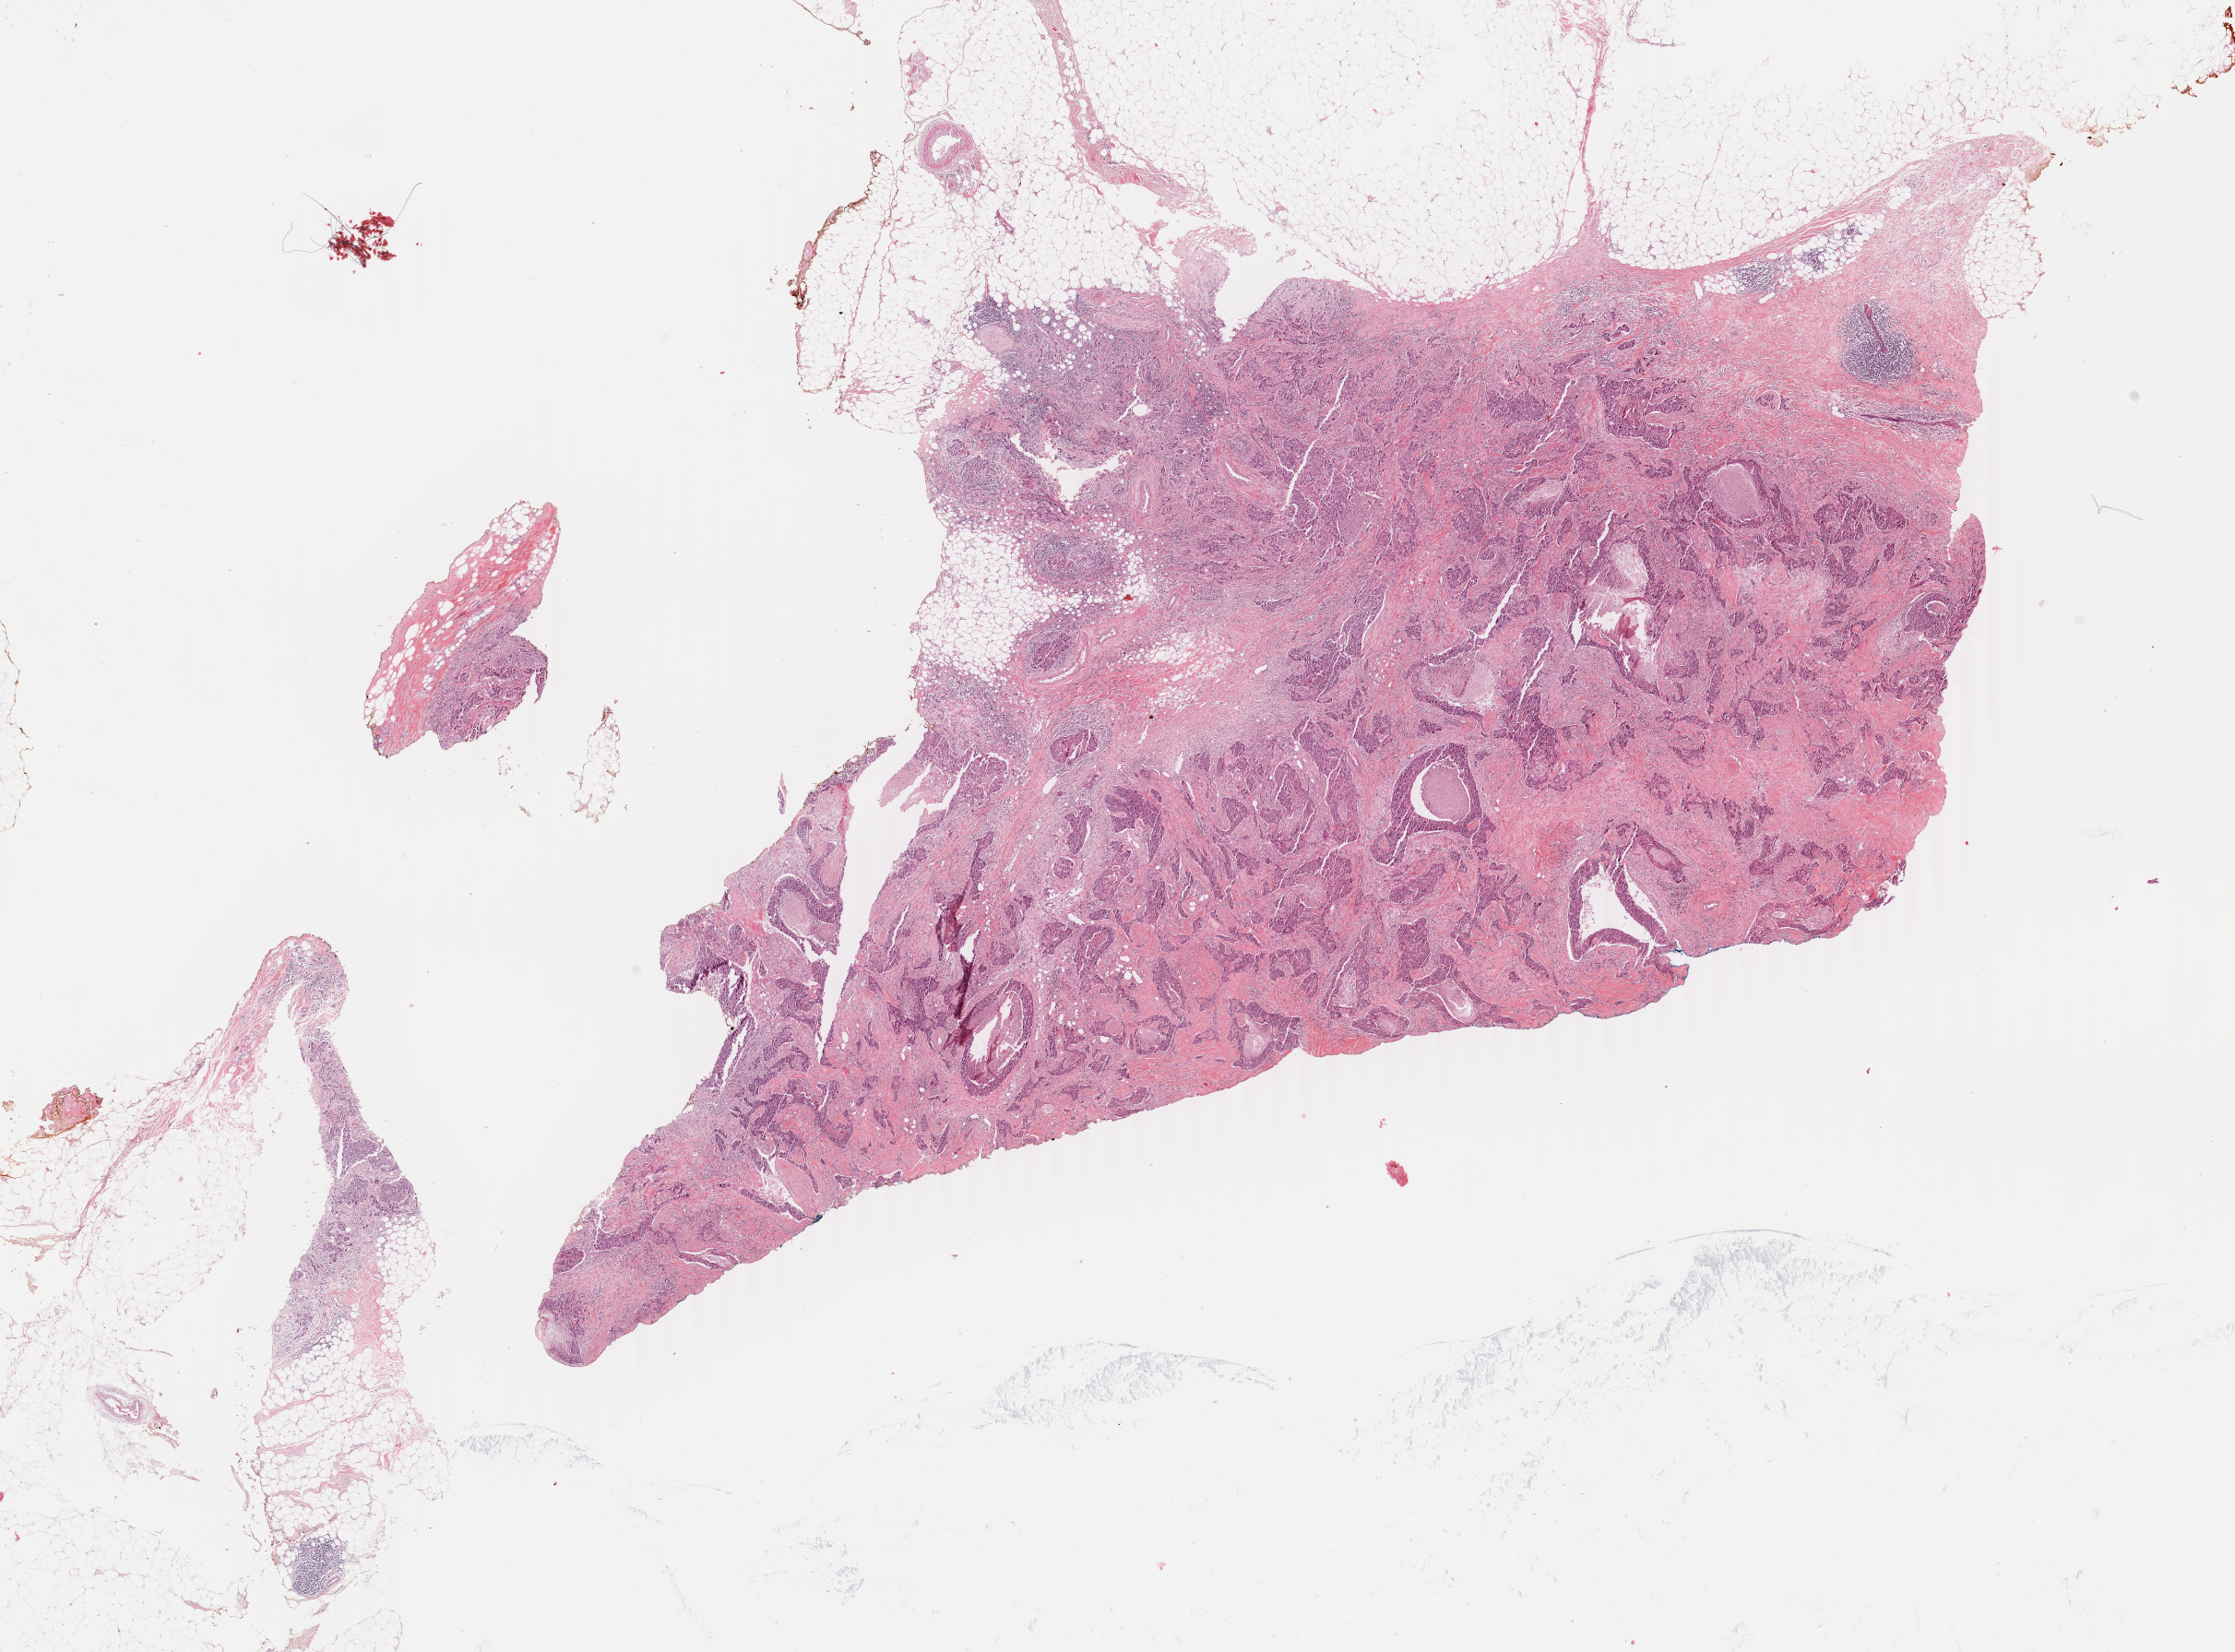
Whole-slide histology image, Hematoxylin and eosin (H&E) stained — a low-resolution overview of the entire scanned area, about 19.3 x 14.2 mm, FFPE section, sample: primary tumour, breast. Female patient; age at initial diagnosis 85 years.
• diagnosis: Infiltrating duct carcinoma, NOS
• AJCC pathologic stage: IIB (7th edition)